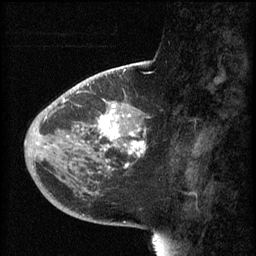
Breast MRI (dynamic contrast-enhanced), one sagittal slice; position 22 of 60 along the scan axis; 3 images stored at this slice position (order not interpretable as contrast timing); 1.5 T; TE 4.2 ms, TR 8.1 ms; 2 mm slice thickness; 256 × 256 image matrix, field of view 200 × 200 mm. Patient: female, 44 years.
Outlined on this slice (semi-automatically segmented with operator editing):
- analysis volume of interest (the breast-tissue region the enhancement analysis was run in; not a lesion): box from (x=59, y=110) to (x=147, y=169) px
- tumour enhancement mask (voxels above the 70 % enhancement threshold inside the analysis volume of interest): (x=73, y=110)–(x=146, y=169)